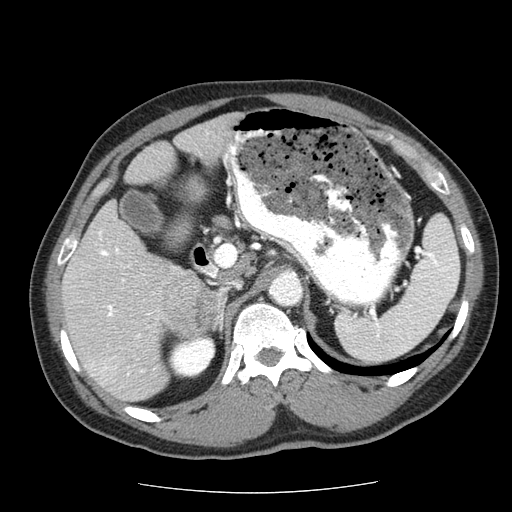
Contrast-enhanced abdominal CT (liver protocol), one axial slice. 120 kVp. Soft-tissue window (W 400 / L 40 HU). 2.5 mm slice thickness. 512 × 512 image matrix, field of view 360 × 360 mm. From the clinical record (not read from this slice): diagnosis: hepatocellular carcinoma (patient treated with transarterial chemoembolisation; whether this scan precedes or follows treatment is not stated here); TNM stage (as recorded): Stage-IIIA; Child-Pugh class: A; tumour differentiation: well differentiated.
Annotated regions visible in this slice (semi-automatically segmented with operator editing):
- liver parenchyma outside the tumour (the mass and vessels are separate outlines, so this box may not span the whole liver): bounding box (x1, y1, x2, y2) in pixels: (60, 112, 242, 400)
- mass: (159, 275, 218, 339)
- liver vessels: (69, 231, 143, 381)